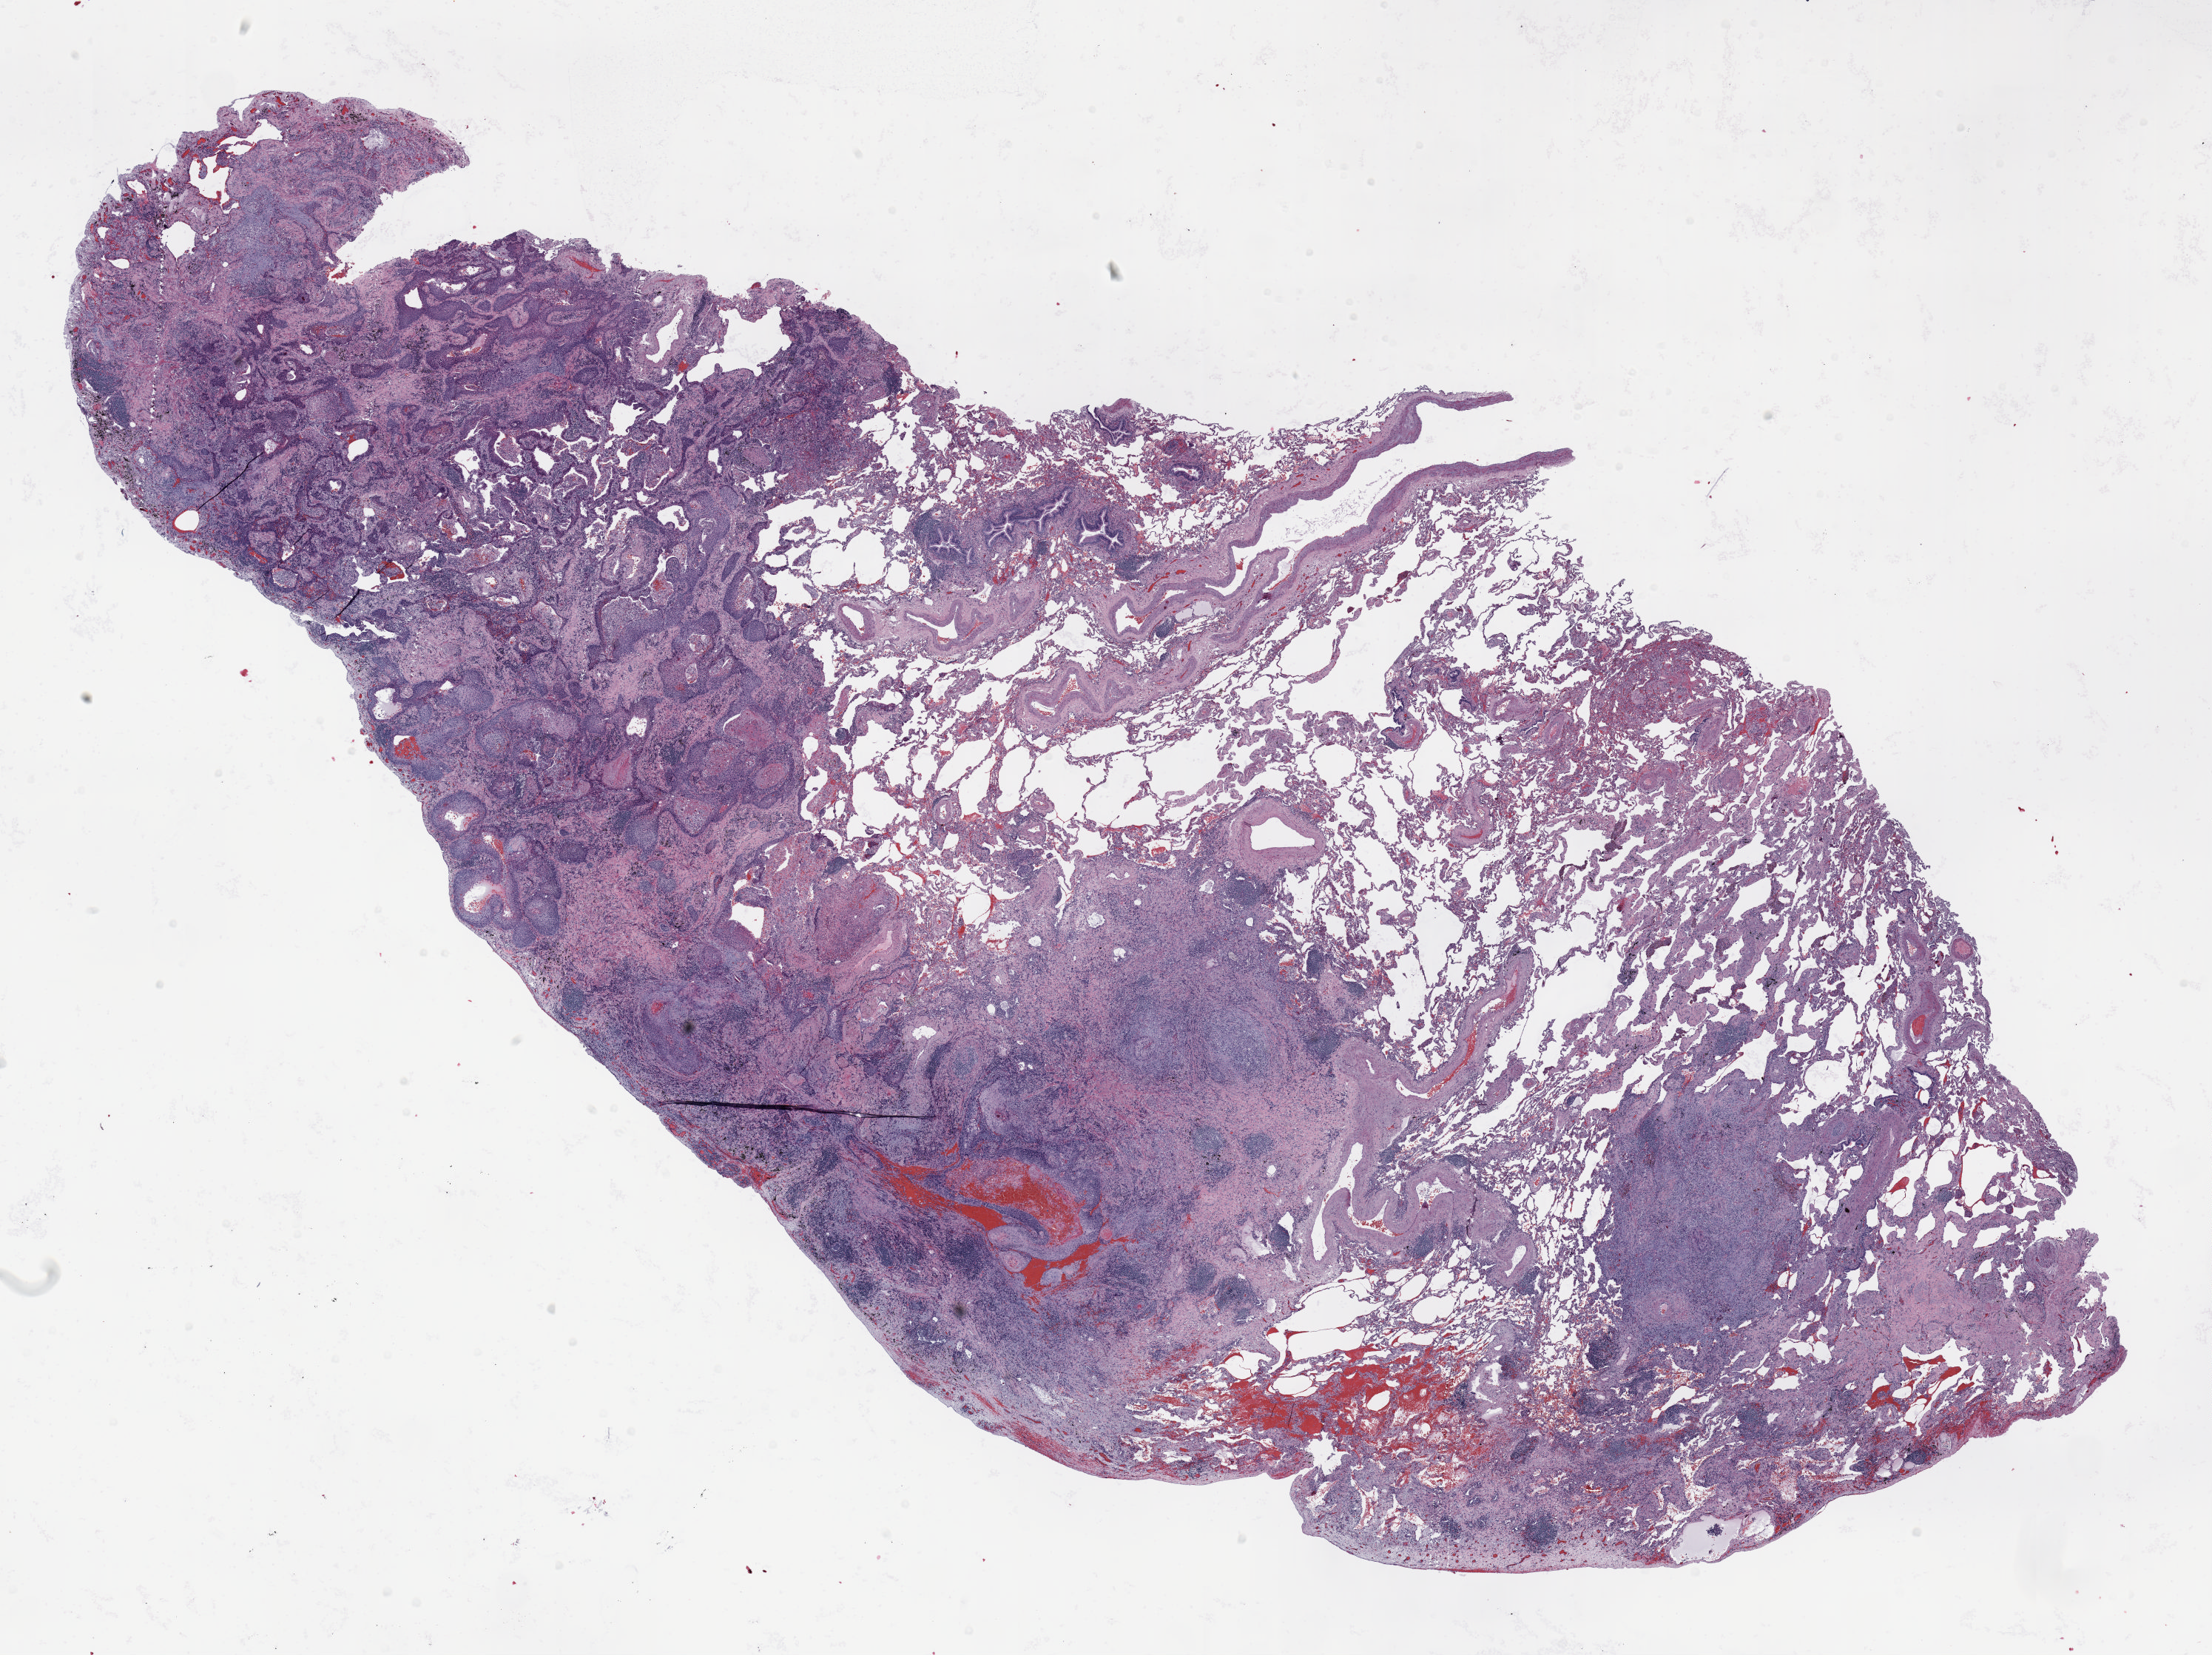
Whole-slide histology image, H&E — a low-resolution overview of the entire scanned area, about 24.0 x 18.0 mm (slide scanned at 20x); FFPE section; lung tissue. Female, age 70 at enrolment. Grade: well differentiated (G1).
ICD-O-3 topography: lower lobe of lung (C34.3). Stage (AJCC 6th edition): IA. Primary tumour location (clinical record): right lower lobe. Participant's lung-cancer diagnosis: Squamous cell carcinoma, NOS (ICD-O-3 8070/3). Tumour size (pathology): 25 mm.